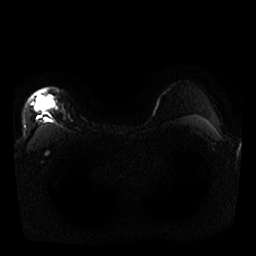
Breast MRI, one axial slice; slice 21 of 25 in the series (ordered by position); diffusion-weighted series; image 2 of 4 stored at this slice position (different b-values; order by instance number); 1.5 T; 4 mm slice thickness; 256 × 256 image matrix, field of view 340 × 340 mm. Female patient.
Outlined on this slice (expert manual segmentation):
- tumour on diffusion-weighted imaging: bounding box [x1, y1, x2, y2] px = [37, 101, 44, 107]